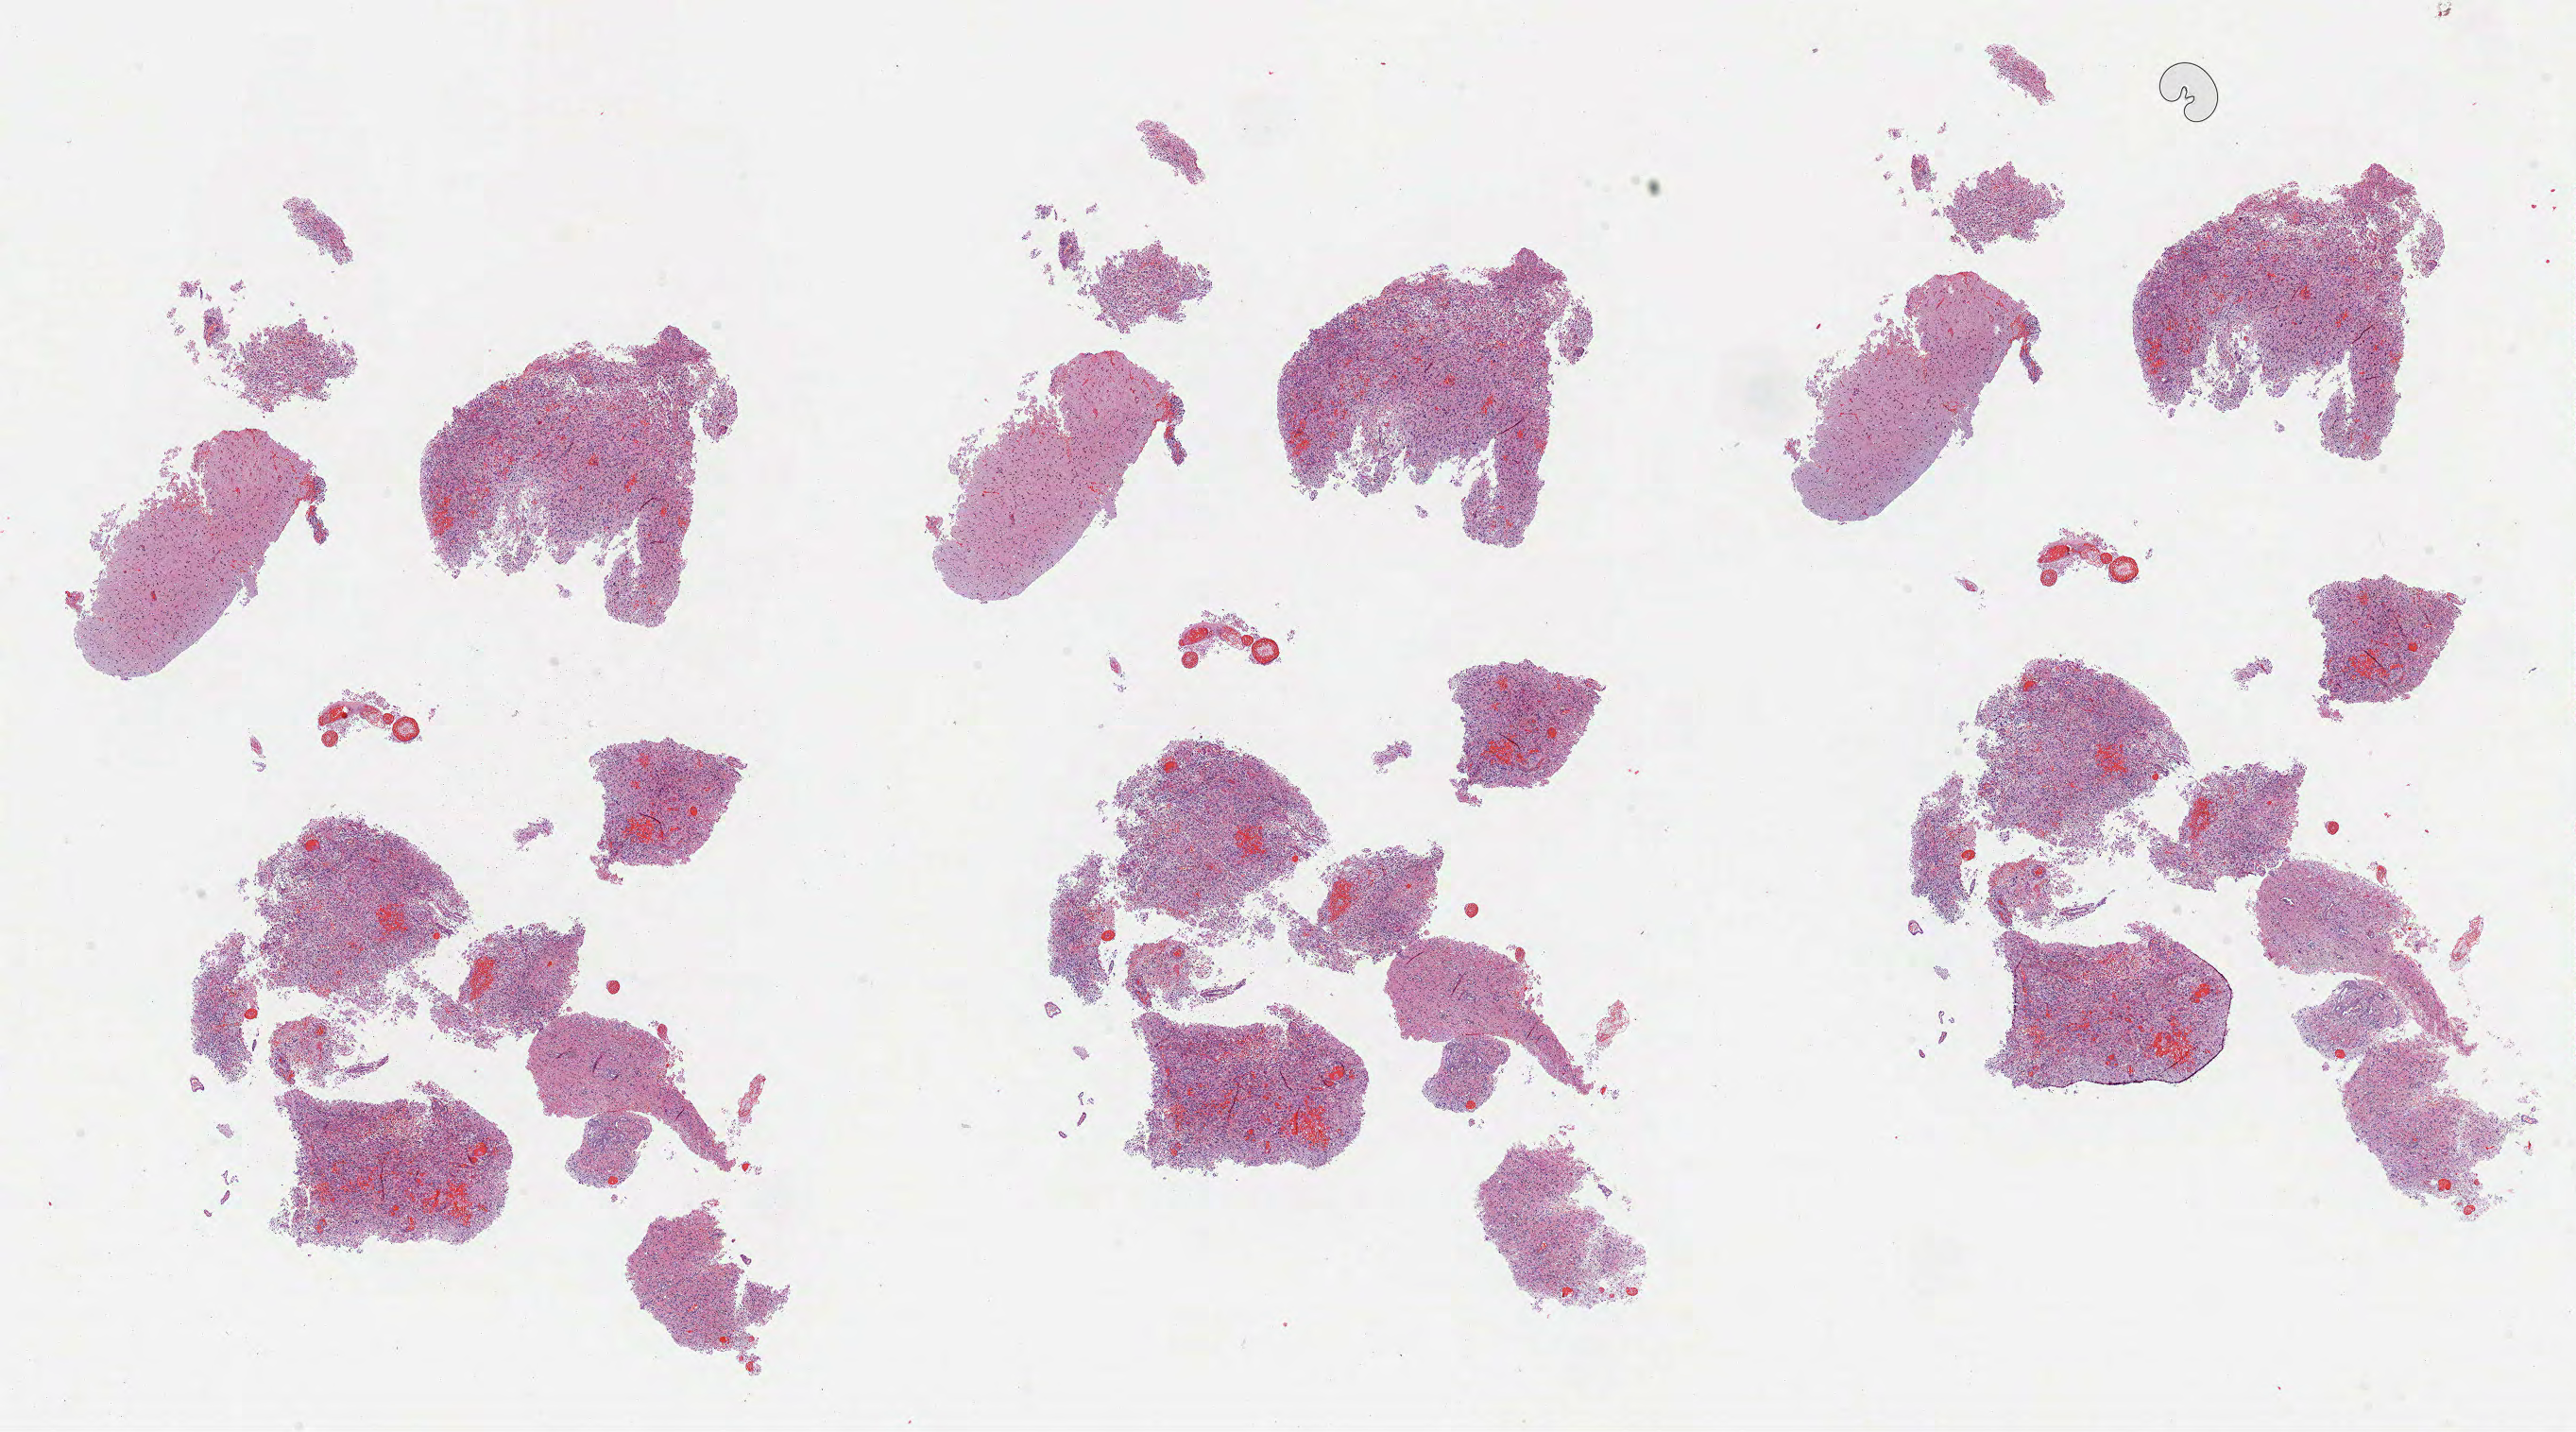
H&E-stained whole-slide image, whole scanned area (about 22.0 x 12.2 mm, slide scanned at 40x) shown as a low-resolution overview; formalin-fixed paraffin-embedded (FFPE) diagnostic section; sample: primary tumour, brain. Male, age 51 years at initial diagnosis.
- pathologic diagnosis: Glioblastoma